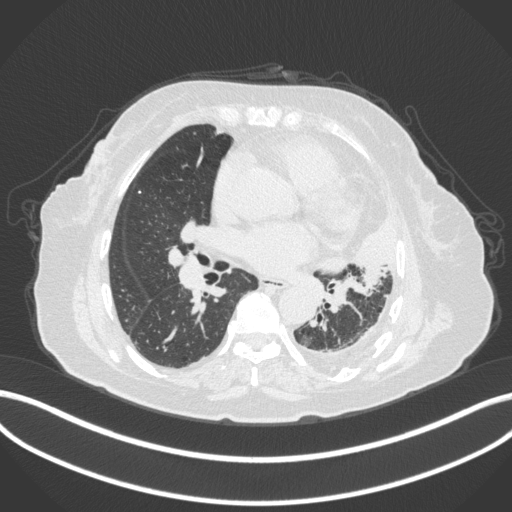
Chest CT, one axial slice; position 181 of 399 along the scan axis; reconstruction kernel B31f; lung window (W 1500 / L -600 HU); 1 mm slice thickness; 512 × 512 image matrix, field of view 400 × 400 mm. Female patient, age 75 years. From the clinical record (not read from this slice): clinical TNM (as recorded): T3 N3 M1.
Outlined on this slice (rectangle marked by the reading radiologist):
- lung tumour (recorded histology: adenocarcinoma): bounding box <317,217,398,282> (left, top, right, bottom; pixels)